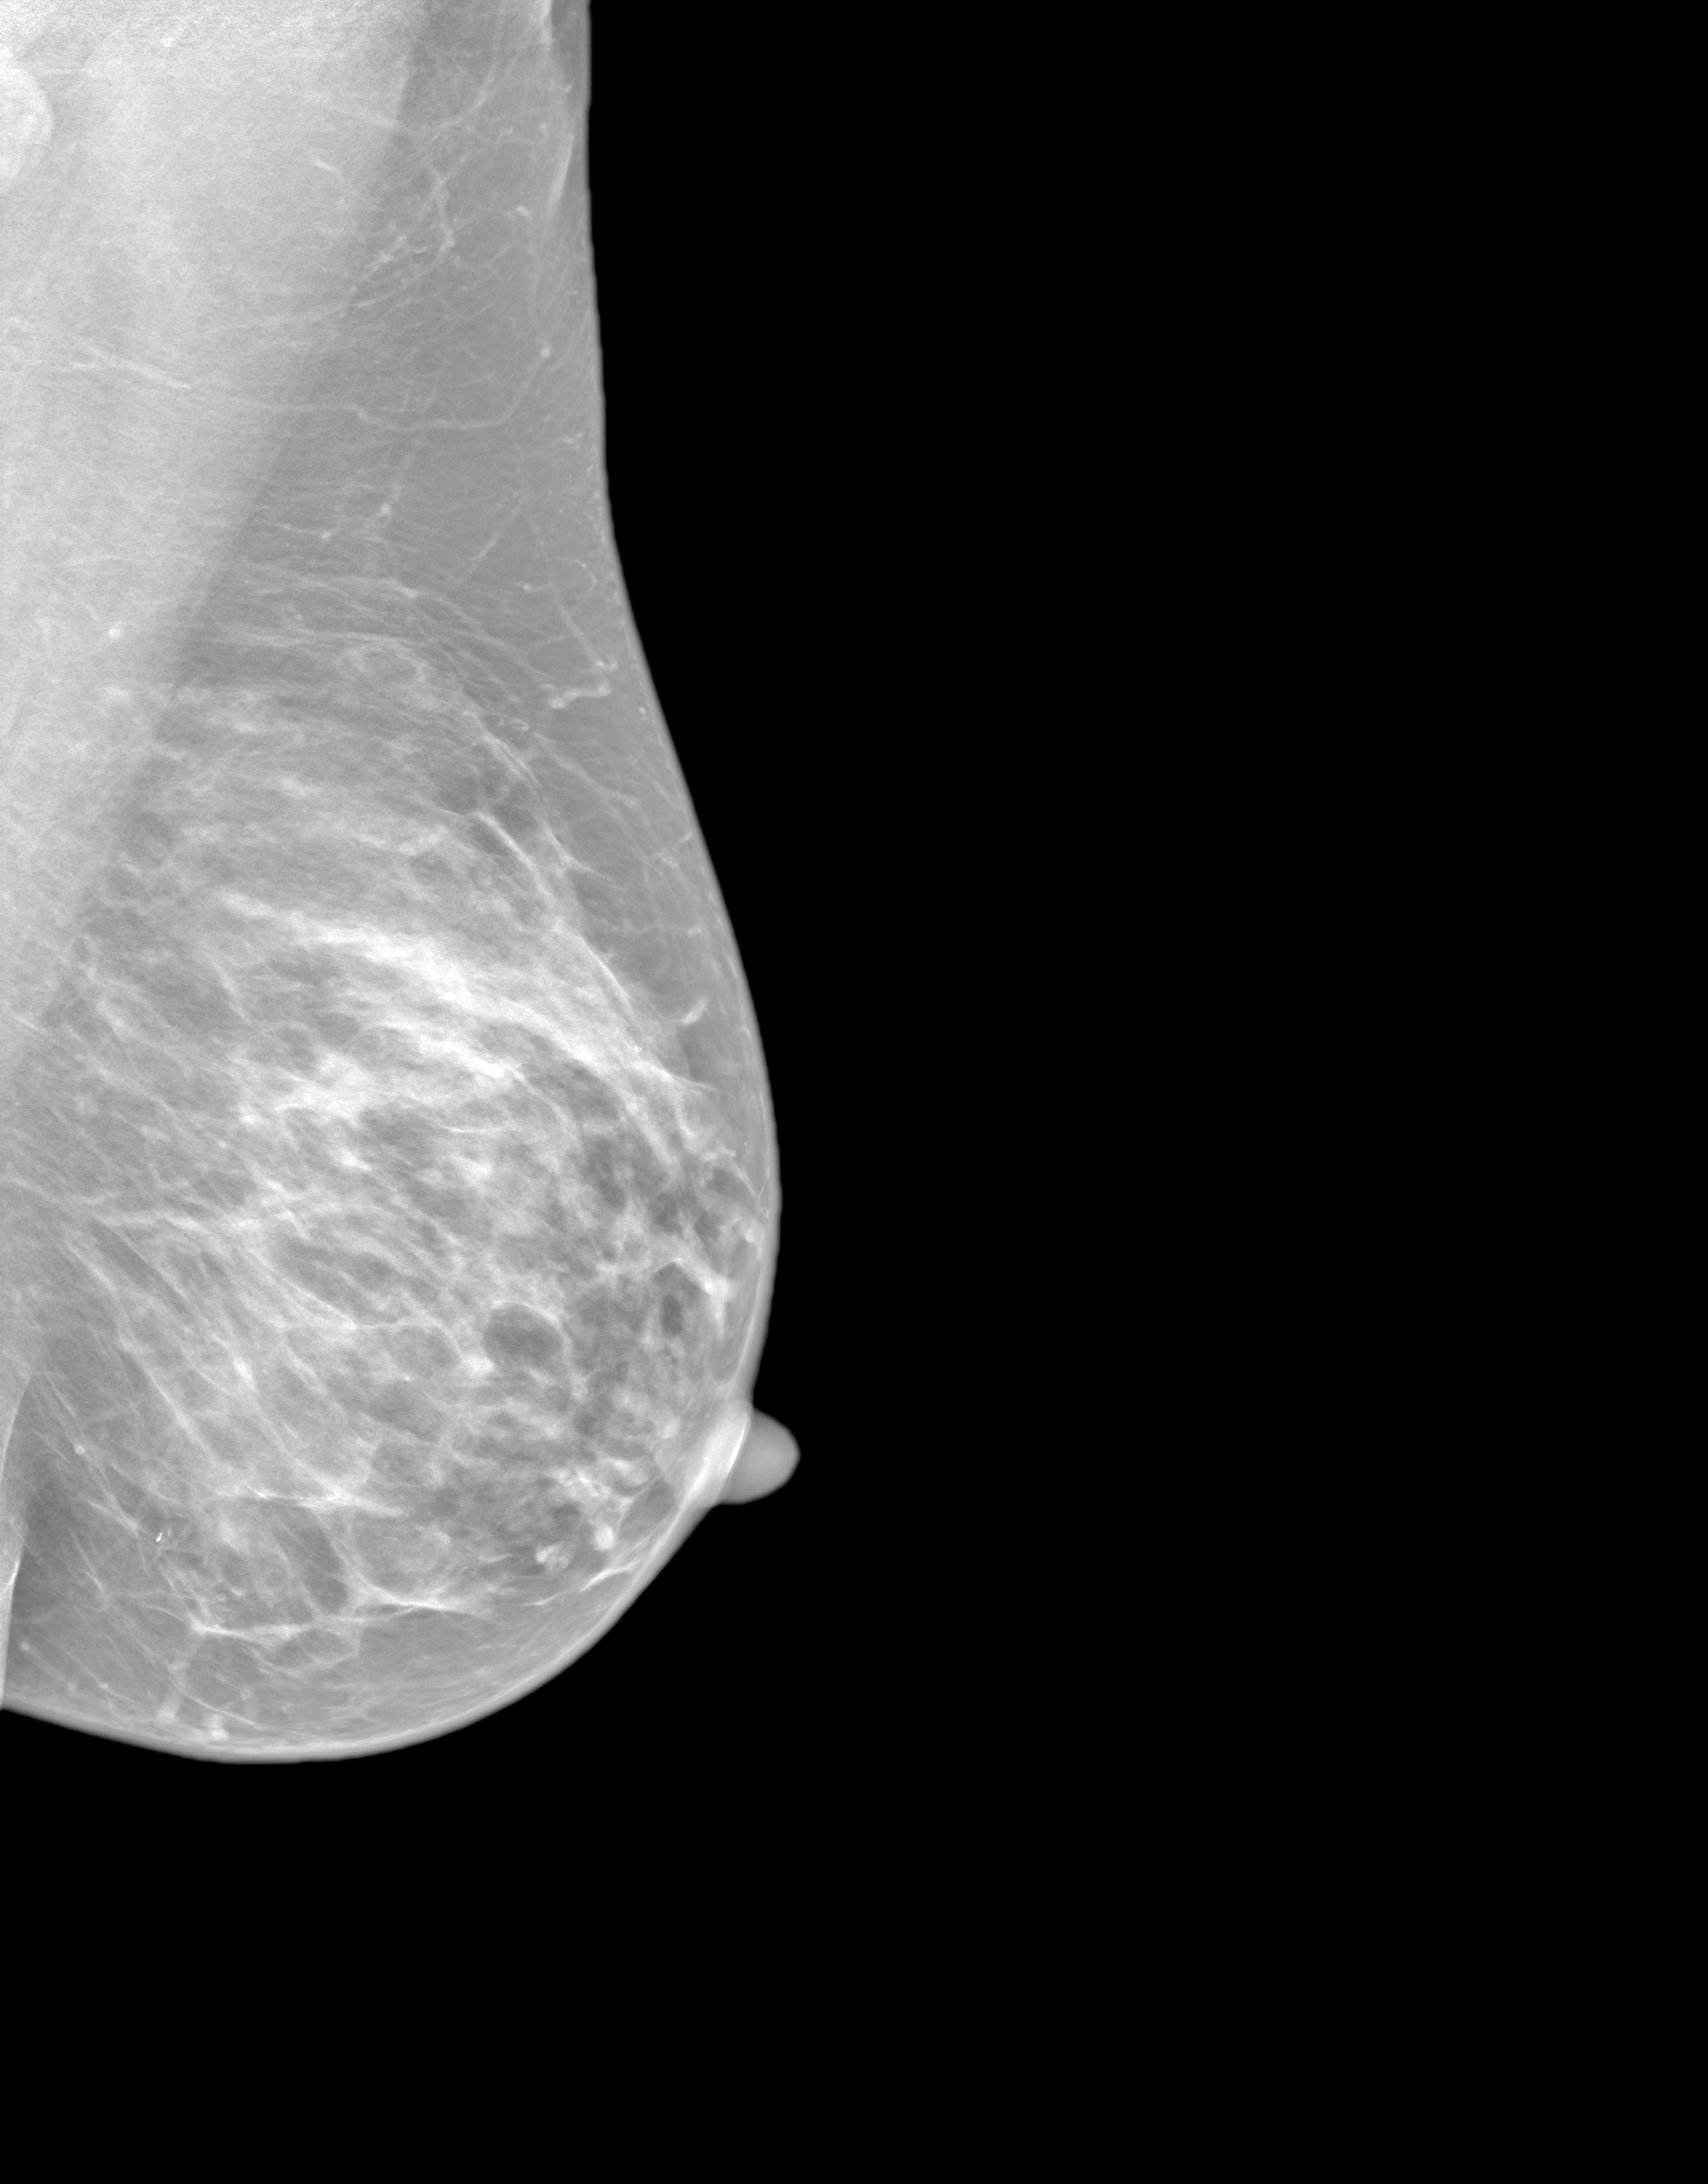
Synthetic 2-D view generated from a tomosynthesis acquisition (not an FFDM exposure), left breast, MLO view, annual screening mammography examination. Female patient, age 49 years.
Final BI-RADS category for the screening round (tomosynthesis exam, both breasts): category 1.